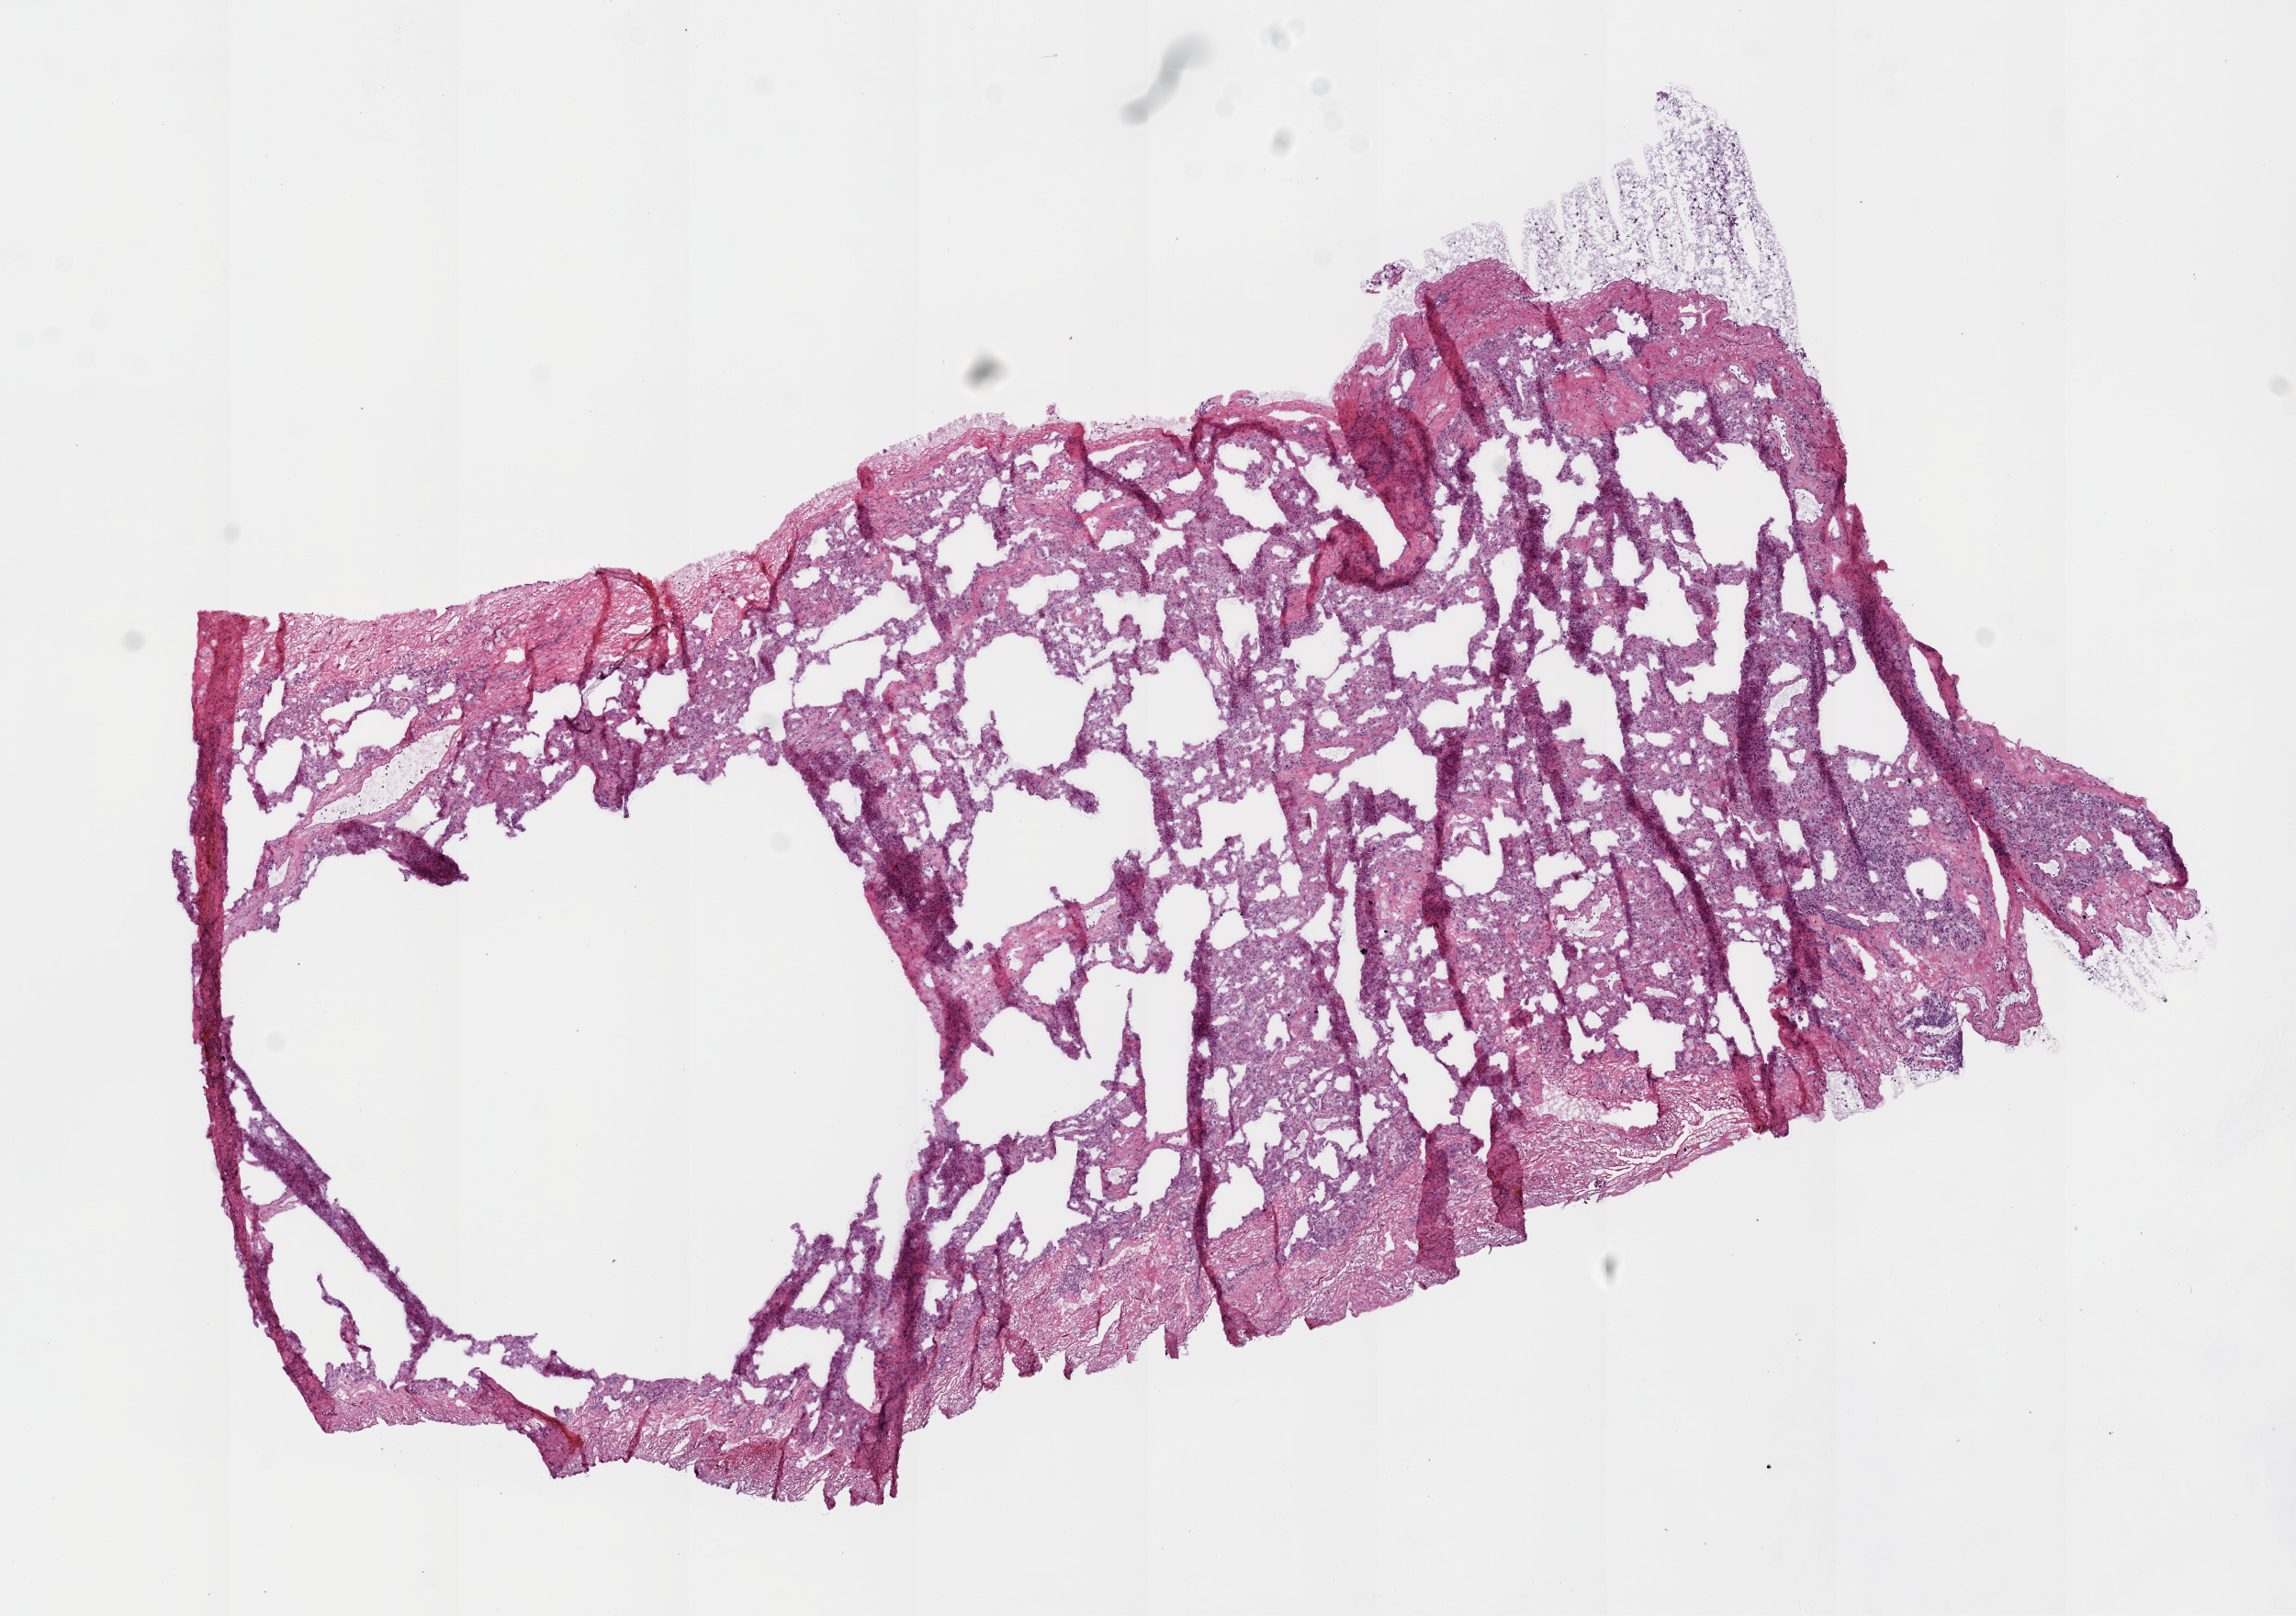
H&E whole-slide image — a low-resolution overview of the entire scanned area, about 10.0 x 7.1 mm (acquisition: 20x scan). Frozen section from the top of the tissue portion. Solid tissue normal (non-tumour tissue) sample from the lung. Female patient; age at initial diagnosis 77 years.
This section: solid tissue normal sample (biorepository sample class). Patient diagnosis: Adenocarcinoma, NOS (lower lobe, lung).